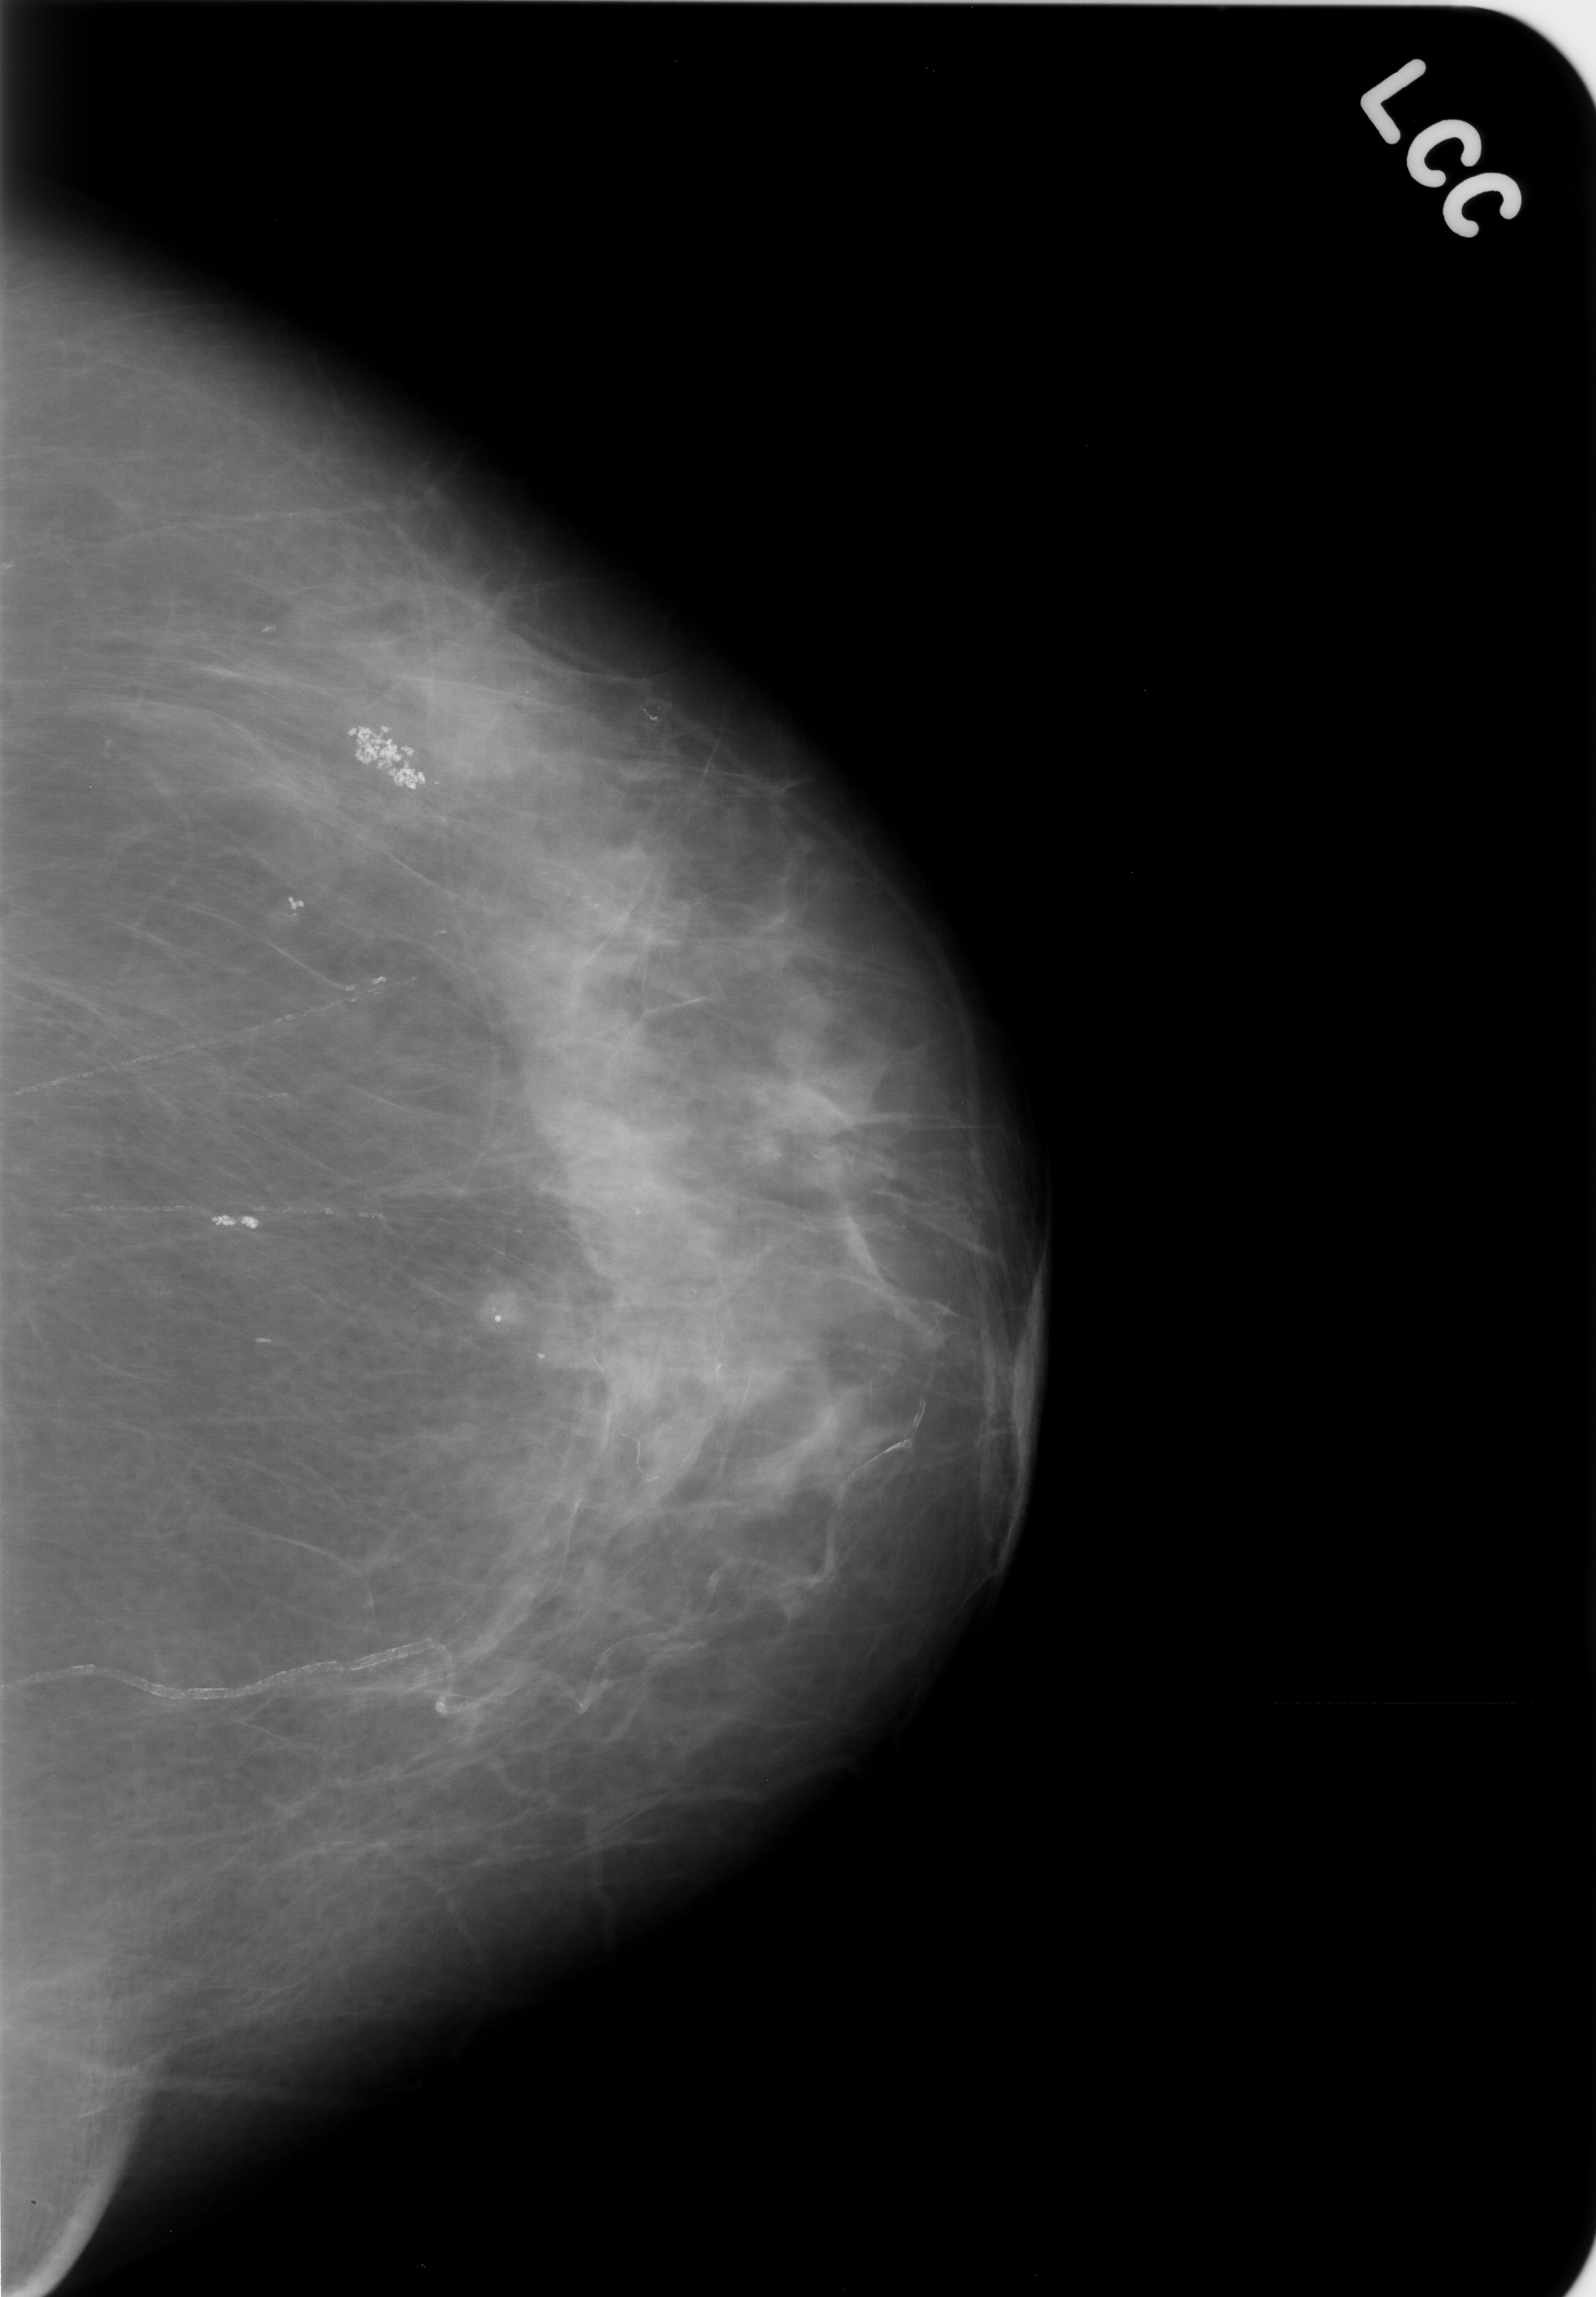
Mammogram (digitized film); left breast; craniocaudal (CC) view; breast composition: scattered fibroglandular densities (BI-RADS density category 2 of 4).
- Abnormality record for this image: Finding 1 of 2: calcifications, morphology amorphous, distribution clustered; BI-RADS assessment category 4; pathology result (as recorded, not read from the image): benign.
- Finding 2 of 2: calcifications, morphology pleomorphic, distribution clustered; BI-RADS assessment category 4; pathology result (as recorded, not read from the image): benign.